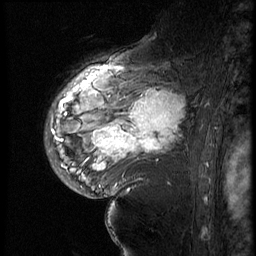
Breast MRI (dynamic contrast-enhanced), one sagittal slice. Position 43 of 60 along the scan axis. 4 images stored at this slice position (order not interpretable as contrast timing). 1.5 T. TE 4.2 ms, TR 9 ms. 2.5 mm slice thickness. 256 × 256 image matrix, field of view 180 × 180 mm. Patient: female, 56 years. From the clinical record (not read from this slice): setting: breast cancer imaged before/during neoadjuvant chemotherapy; receptor status: HER2-positive.
Outlined on this slice (semi-automatic segmentation, software-assisted and operator-edited):
- analysis volume of interest (the breast-tissue region the enhancement analysis was run in; not a lesion): box from (x=82, y=83) to (x=199, y=177) px
- tumour enhancement mask (voxels above the 140 % enhancement threshold inside the analysis volume of interest): (x=93, y=90)–(x=186, y=171)